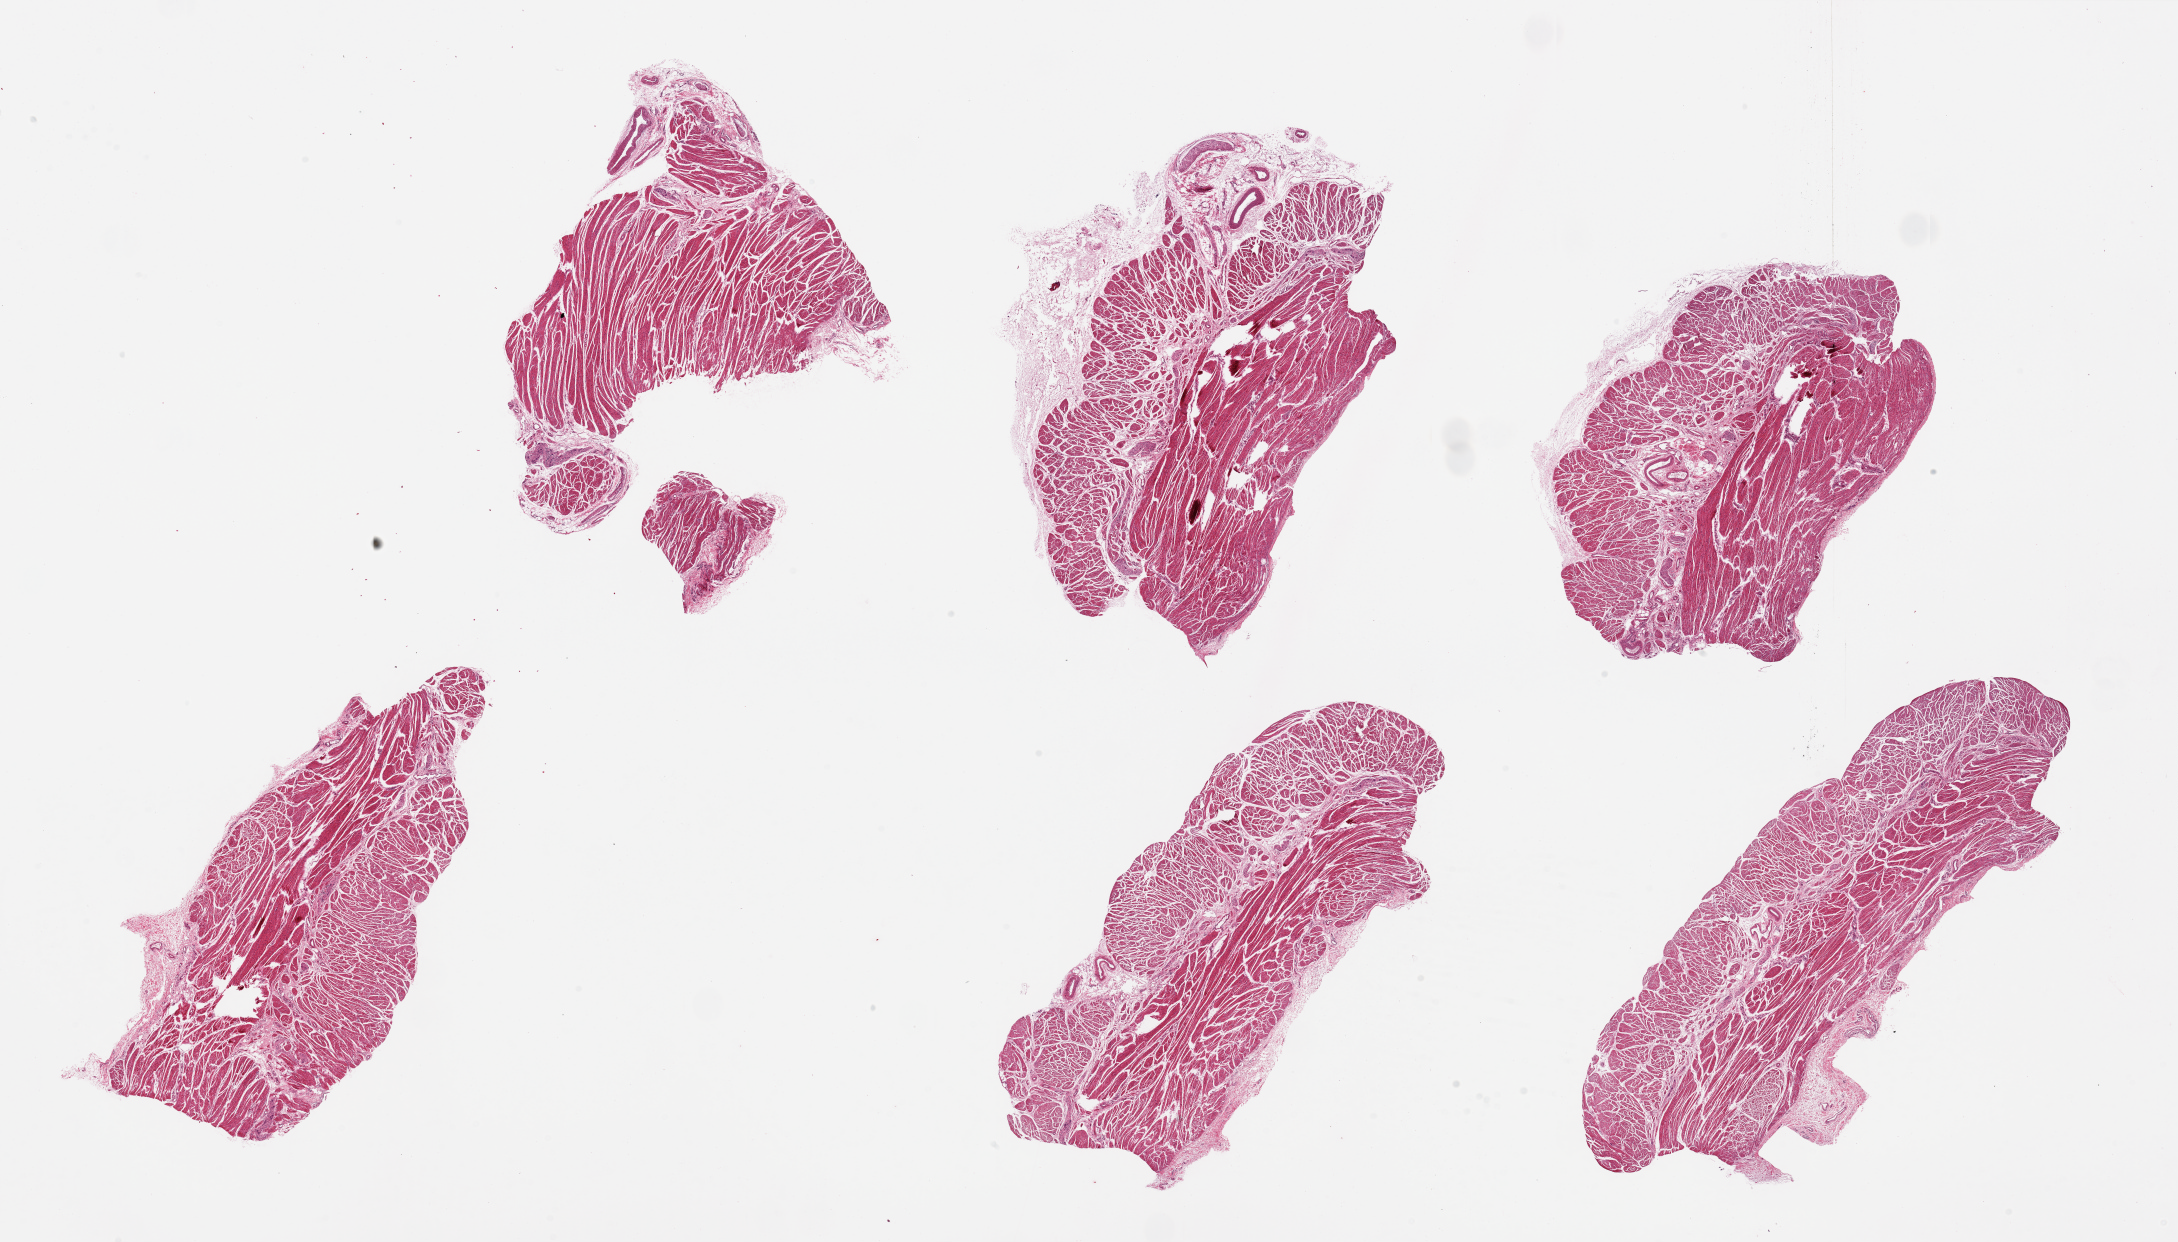
Whole-slide image, H&E stain — a low-resolution overview of the entire scanned area, about 34.5 x 19.6 mm. PAXgene-fixed paraffin-embedded (PFPE) section. Sampled site (target tissue): gastroesophageal junction. Tissue donor sample. Male donor.
- reviewer comment on this tissue sample: 6 pieces, ranging from 7x5 to 10x4mm; muscularis, good specimens